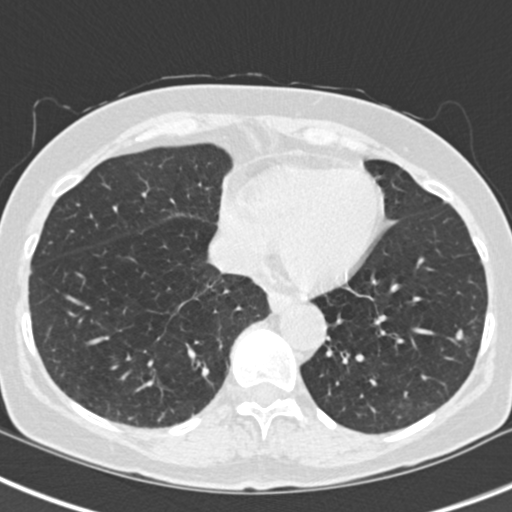
Low-dose screening chest CT, one axial slice; position 76 of 229 along the scan axis; 120 kVp; lung window (W 1500 / L -600 HU); 2 mm slice thickness; 512 × 512 image matrix.
Structures marked on this image (manually delineated by an expert):
- lesion 1 (tumor): bounding box [x1, y1, x2, y2] px = [455, 329, 464, 341]